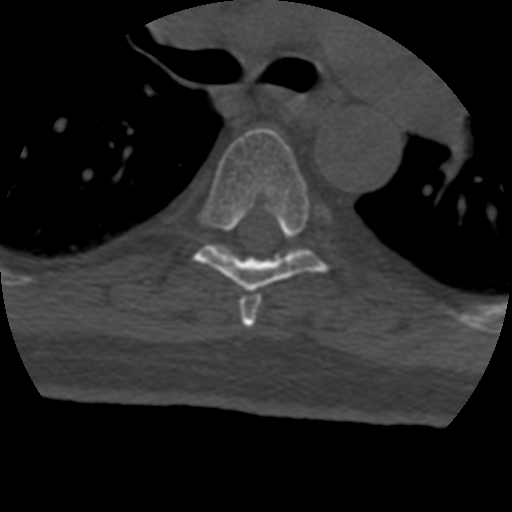
CT including the spine, one axial slice. Position 300 of 399 along the scan axis. Reconstruction kernel STANDARD. Bone window (W 1800 / L 400 HU). 1.25 mm slice thickness. 512 × 512 image matrix. Patient age 69 years. Case-level facts recorded for this patient, not image findings: primary cancer: prostate.
Outlined on this slice (semi-automatically segmented with operator editing):
- T5 vertebra: box from (x=239, y=288) to (x=262, y=327) px
- T6 vertebra: (x=194, y=128)–(x=327, y=292)
- T7 vertebra: (x=213, y=244)–(x=299, y=257)